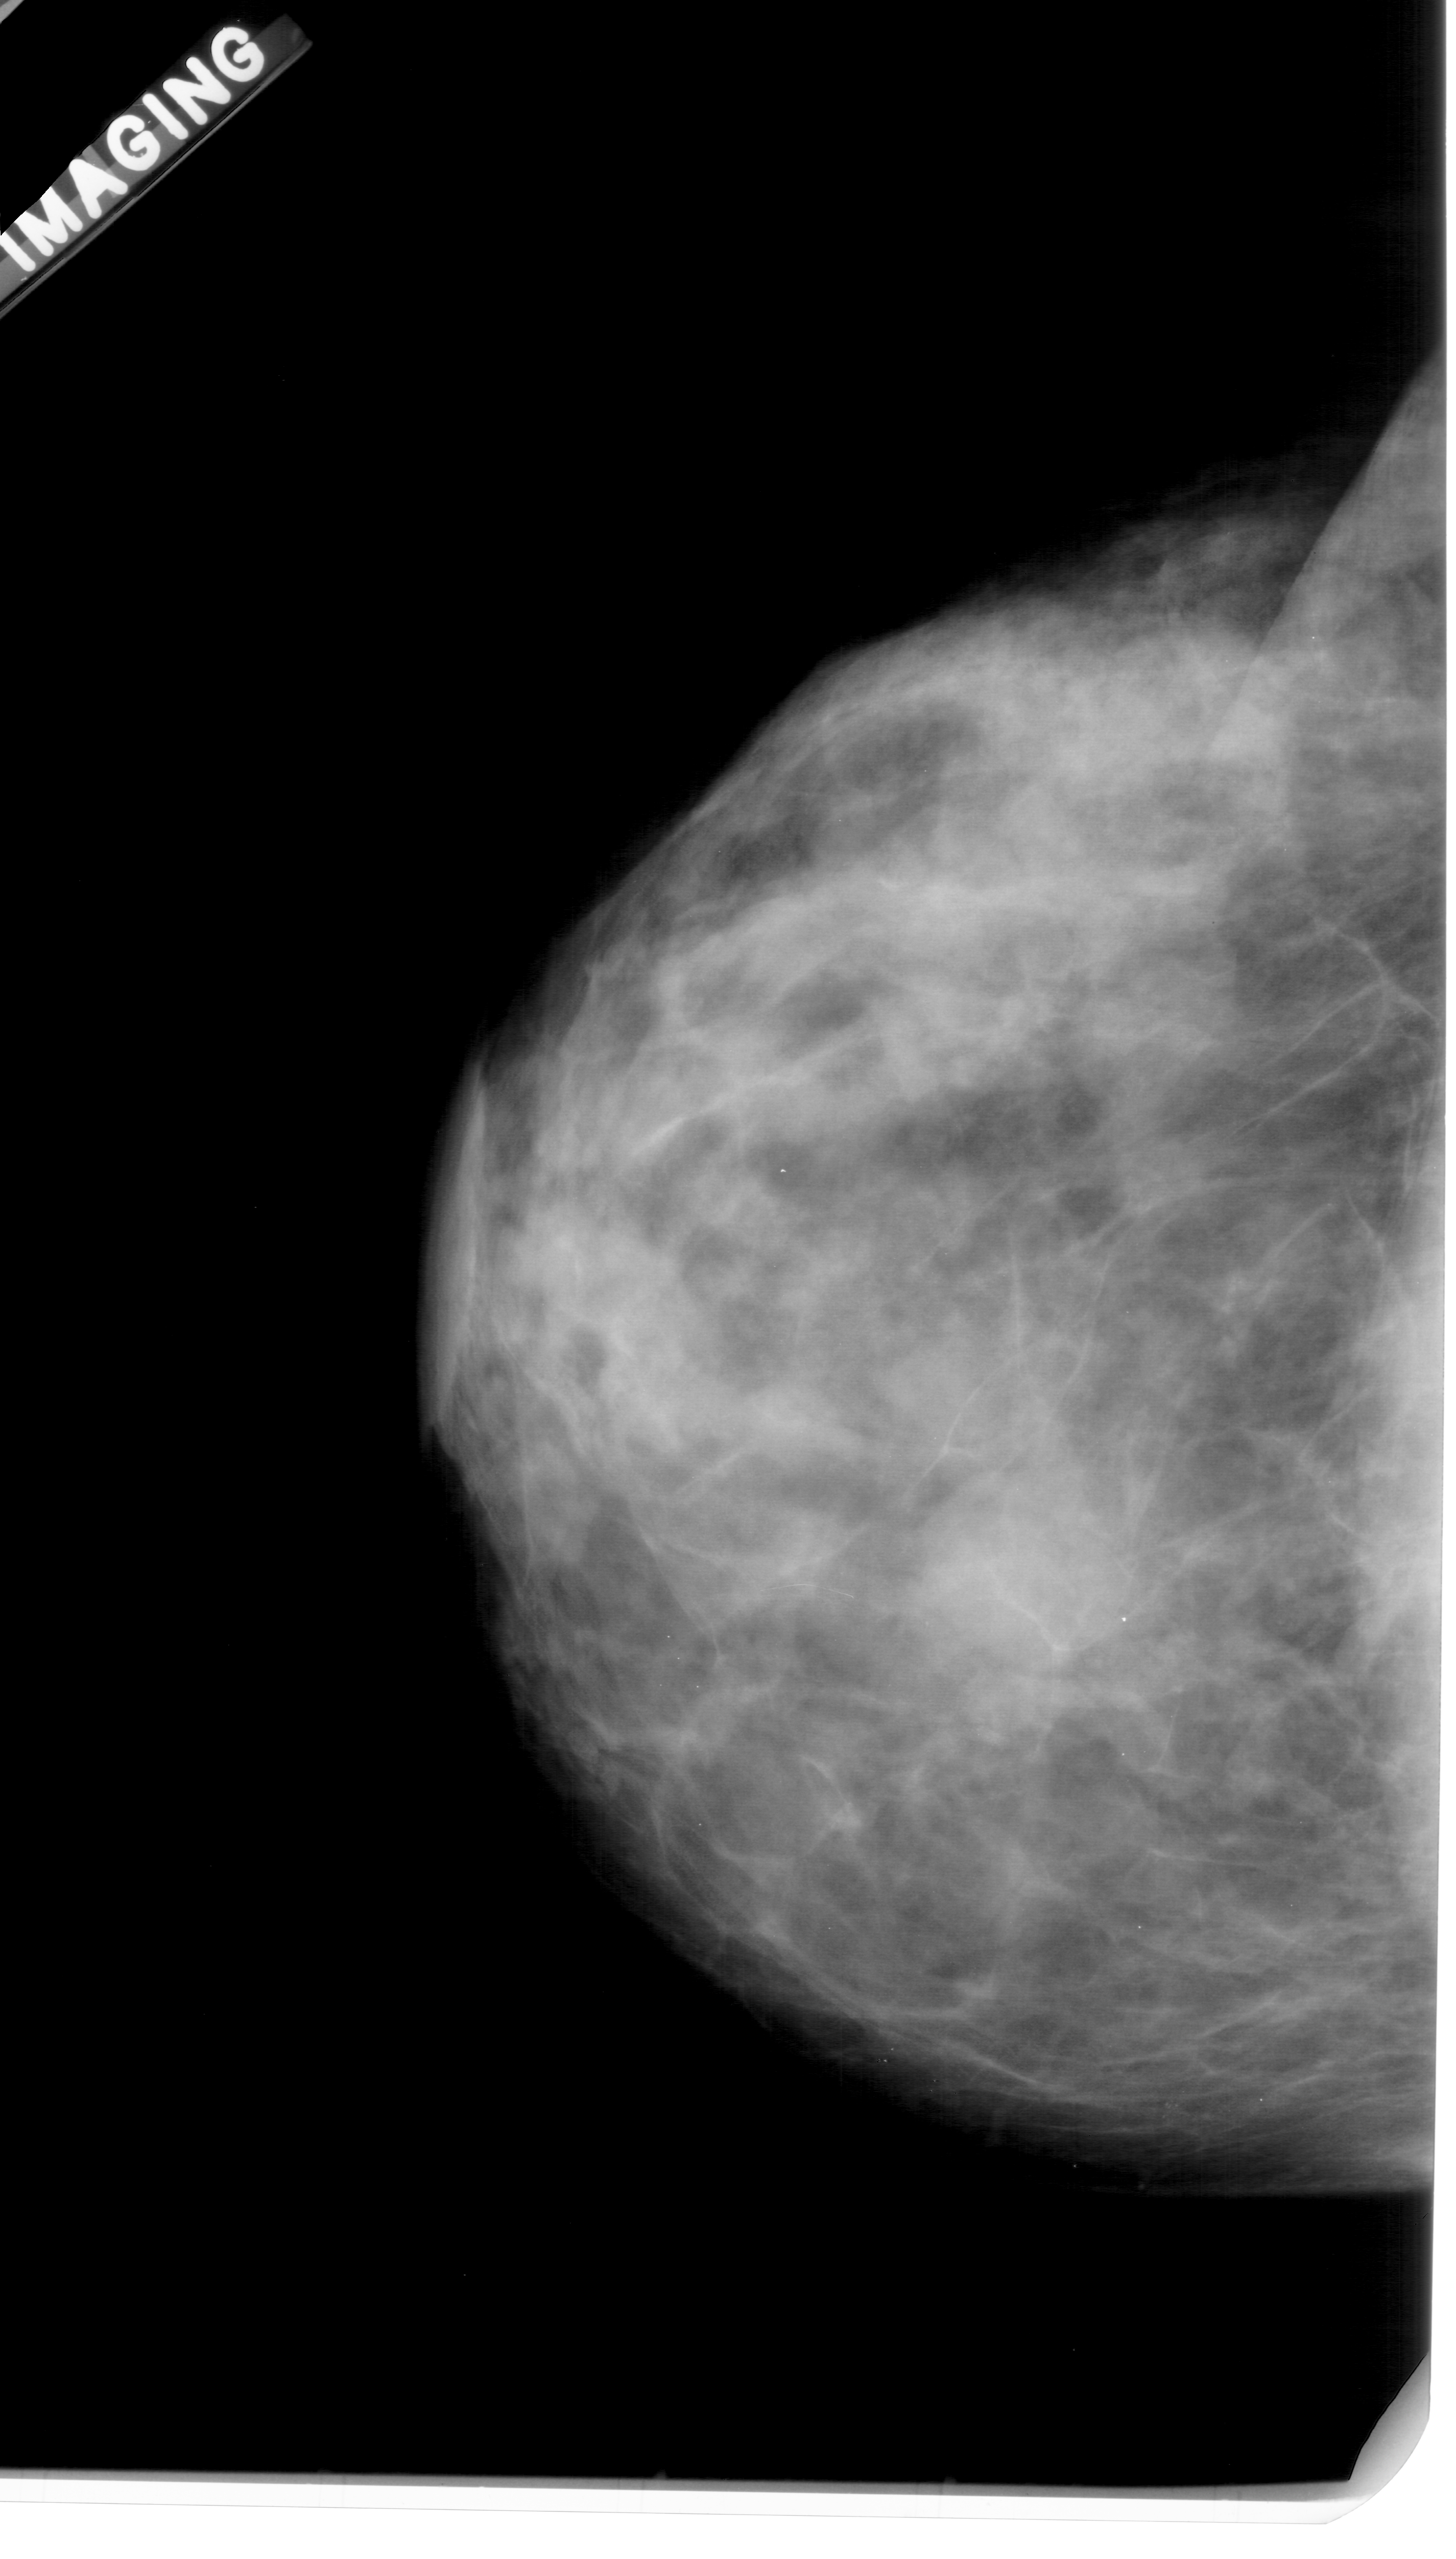
Scanned film-screen mammogram. Left breast. CC view. BI-RADS breast density category 4 (scale 1–4). 1456 × 2559 image matrix.
Expert-marked regions of interest on this film, with their recorded descriptors:
- mass, shape oval, margins obscured; BI-RADS assessment category 3; pathology result (as recorded, not read from the image): benign: bounding box <898,1473,1105,1670> (left, top, right, bottom; pixels)